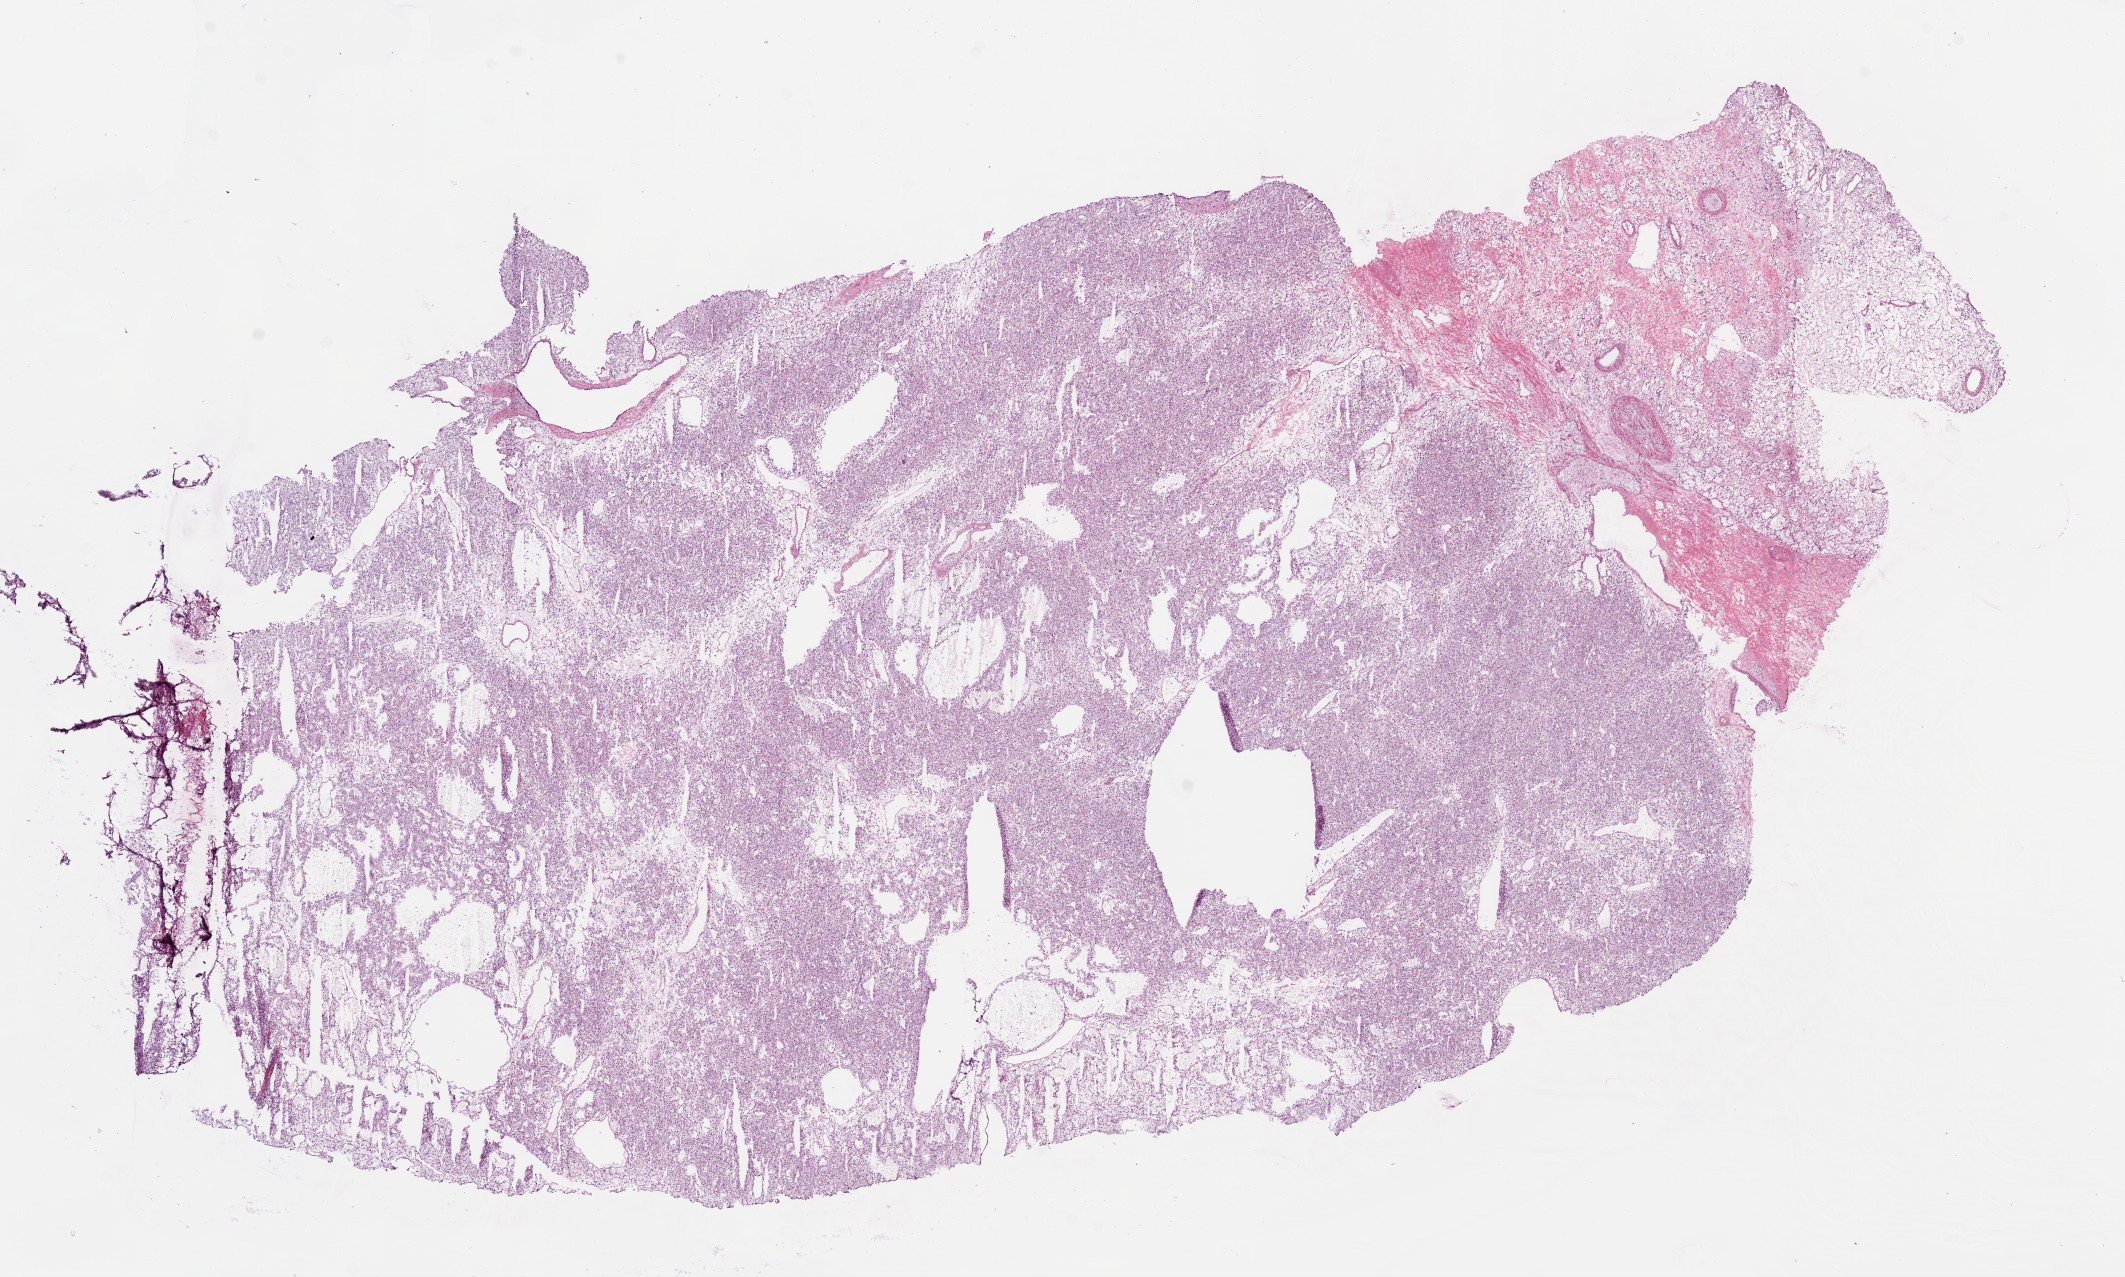
H&E whole-slide image, shown as a low-resolution overview of the whole scanned area (about 17.1 x 10.2 mm, acquisition: 20x scan). Frozen section from the bottom of the tissue portion. Sample: primary tumour, kidney. Female, age 43 years at initial diagnosis. Histologic grade: G3 (poorly differentiated). Composition of this section per pathologist review: tumour cells 95%, tumour nuclei 95%, stromal cells 5%, necrosis 0%. Infiltration values recorded for this section: lymphocyte infiltration 1%.
• AJCC pathologic stage: I
• histologic diagnosis: Clear cell adenocarcinoma, NOS